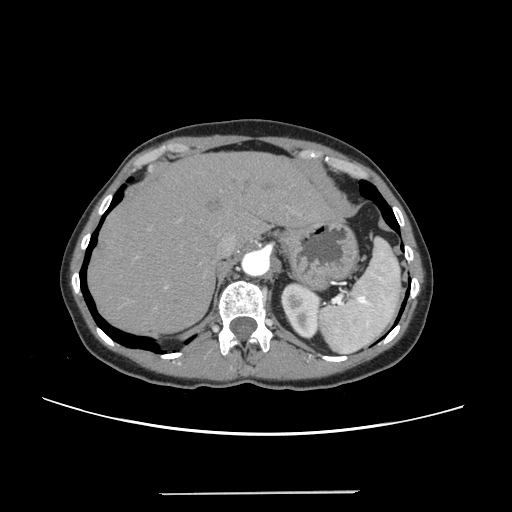
Contrast-enhanced abdominal CT, one axial slice; slice 189 of 240 in the series (ordered by position); intravenous contrast given; soft-tissue window (W 400 / L 40 HU); 512 × 512 image matrix, field of view 371 × 371 mm. Female patient, age 60 years. Case-level facts recorded for this patient, not image findings: diagnosis: colorectal cancer liver metastases, imaged before liver resection; multiple liver metastases: no; largest metastasis: 1.5 cm; disease in both lobes: no.
Outlined on this slice (expert manual segmentation):
- hepatic veins: bounding box [x1, y1, x2, y2] px = [220, 235, 235, 254]
- liver: [89, 153, 335, 334]
- planned liver remnant (the part of the liver to remain after resection): [89, 153, 335, 335]
- portal vein (with intrahepatic branches): [166, 218, 180, 288]